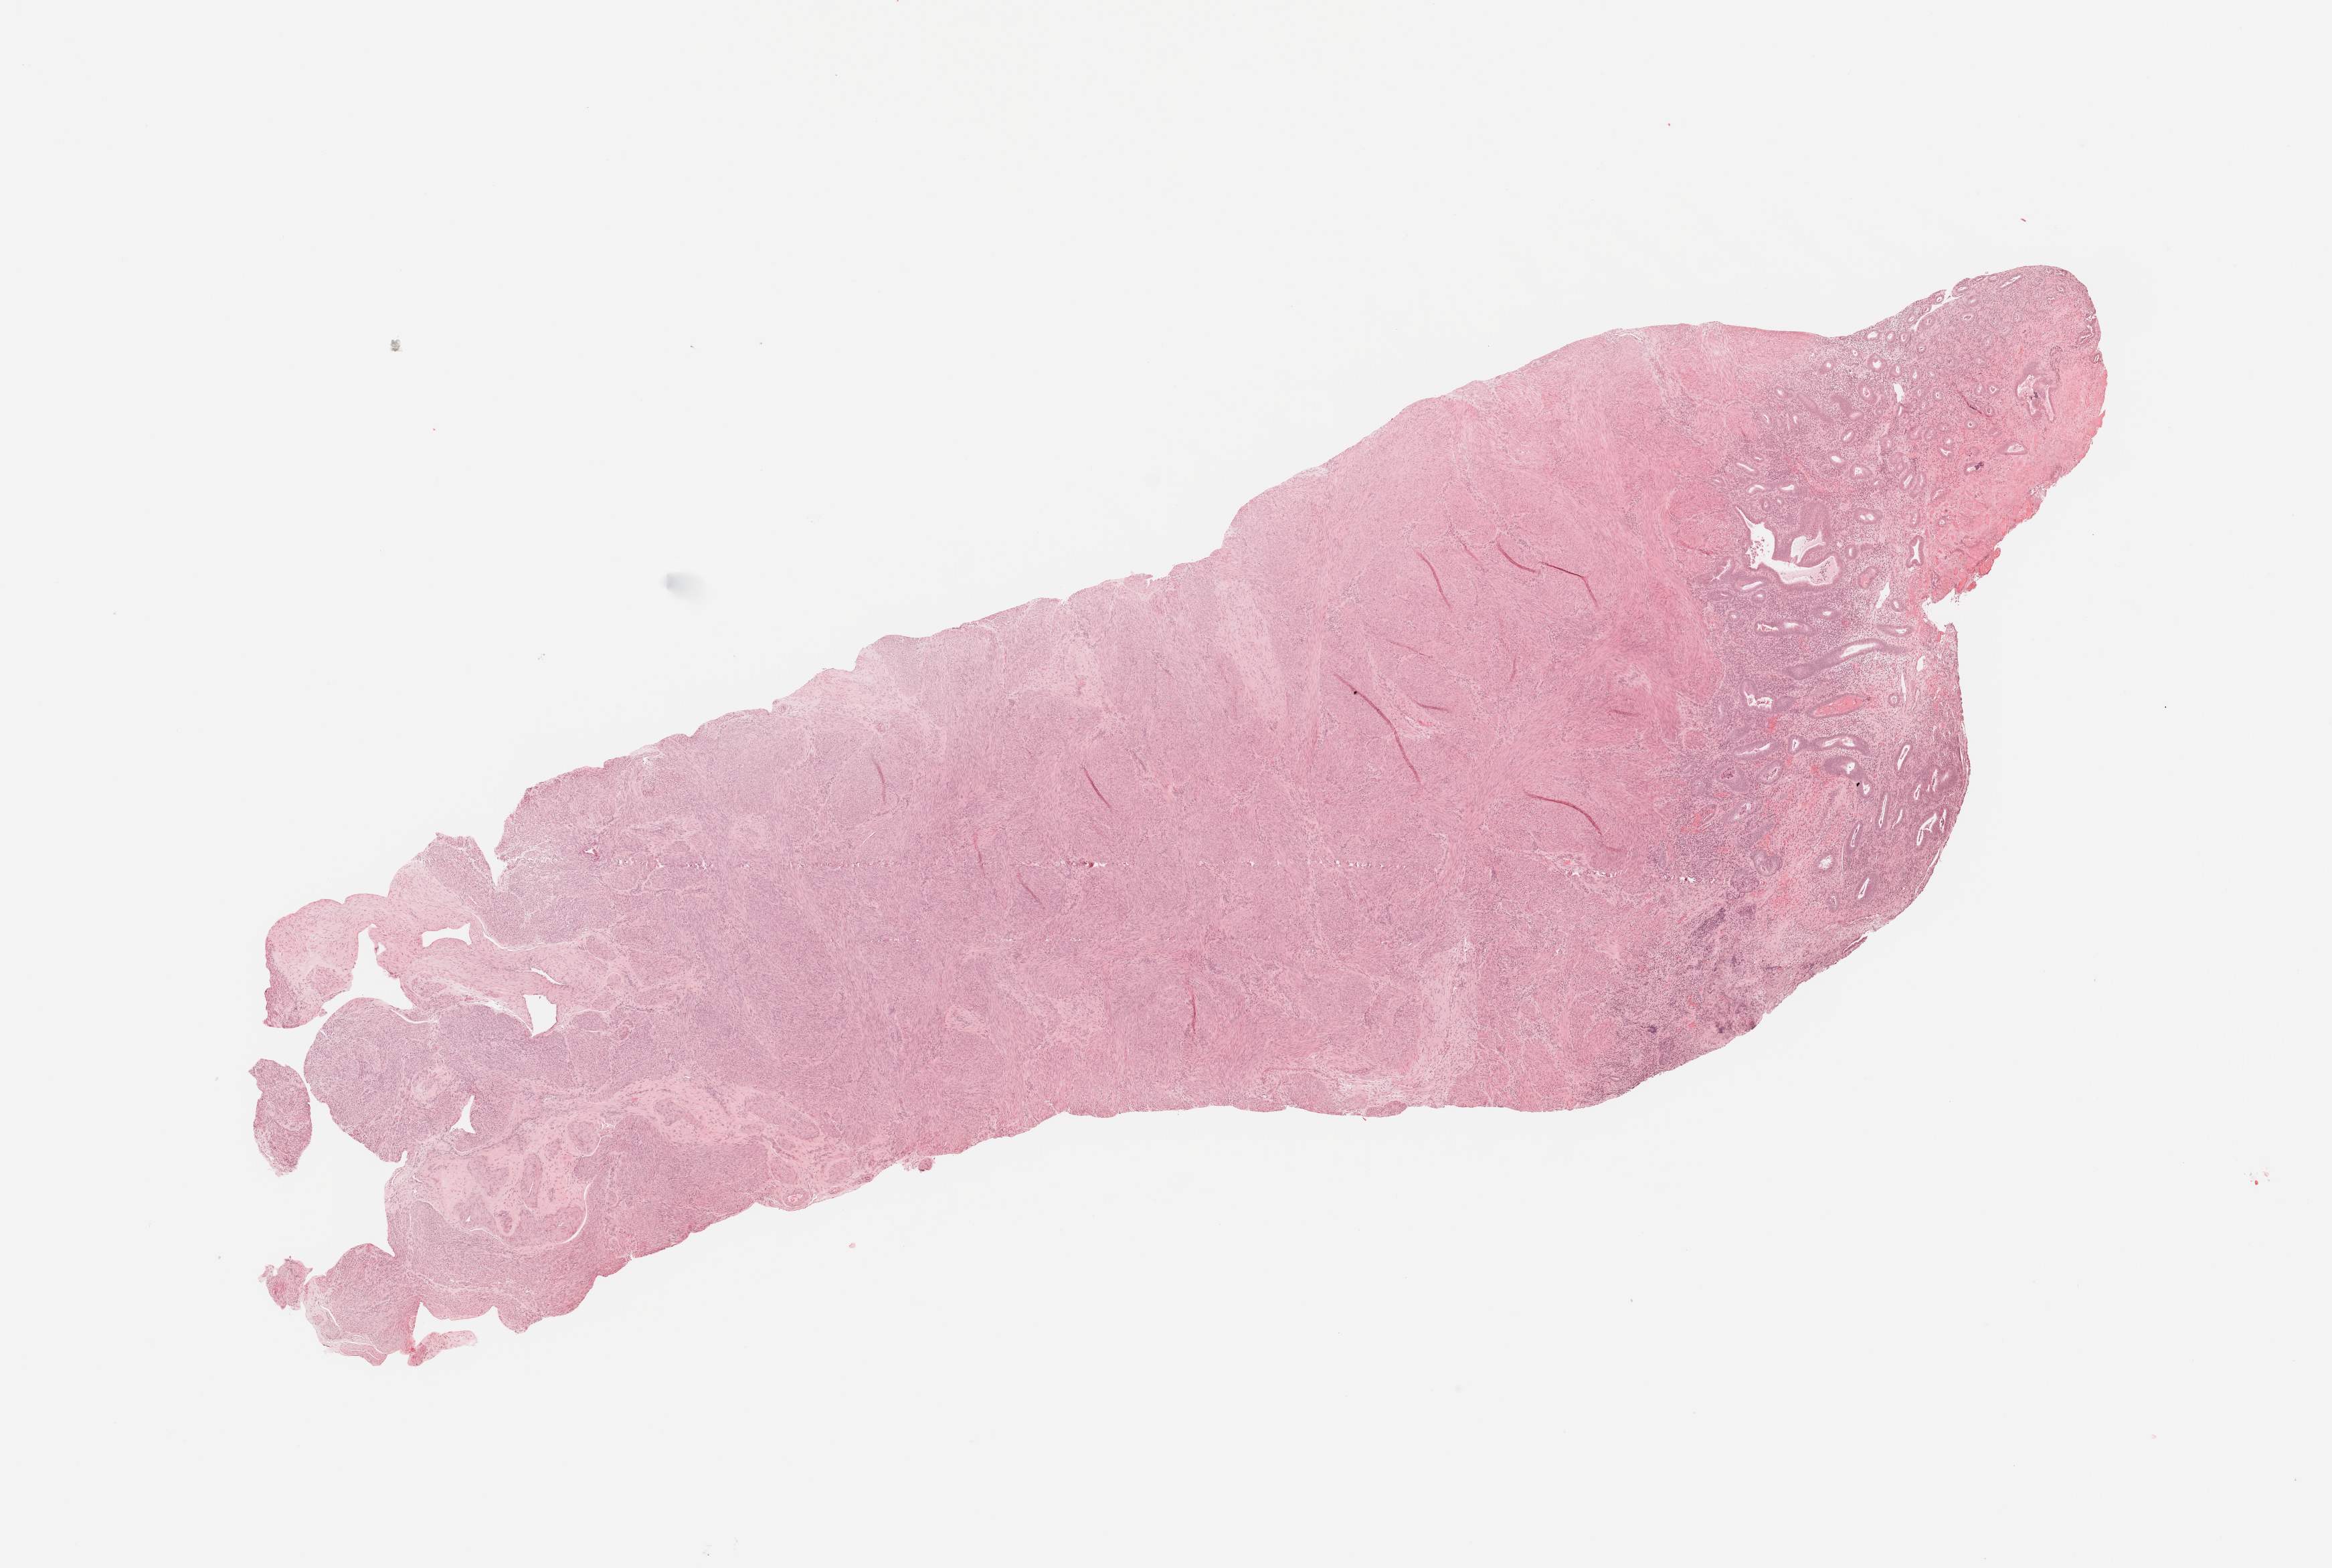
Digitized H&E tissue section (whole slide) — whole scanned area (about 13.8 x 9.3 mm, acquisition: 20x scan) shown as a low-resolution overview. Uterus, normal (non-tumour) tissue. Female, 56 y/o.
This section: normal (non-tumour) tissue from the same patient. Patient diagnosis: Endometrioid adenocarcinoma, NOS.